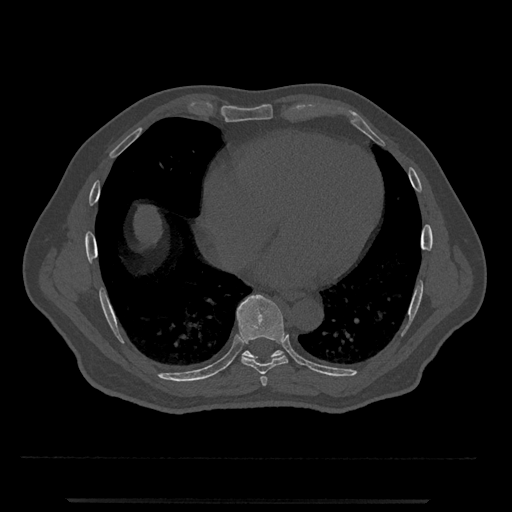
CT including the spine, one axial slice. Position 613 of 797 along the scan axis. Reconstruction kernel Br40s/3. 120 kVp. Bone window (W 1800 / L 400 HU). 0.5 mm slice thickness. 512 × 512 image matrix, field of view 419 × 419 mm. Male patient, age 63 years. From the clinical record (not read from this slice): primary cancer: prostate.
Structures marked on this image (semi-automatically segmented with operator editing):
- T7 vertebra: bounding box [x1, y1, x2, y2] px = [260, 376, 268, 386]
- T8 vertebra: [236, 295, 288, 375]
- T9 vertebra: [242, 350, 284, 361]